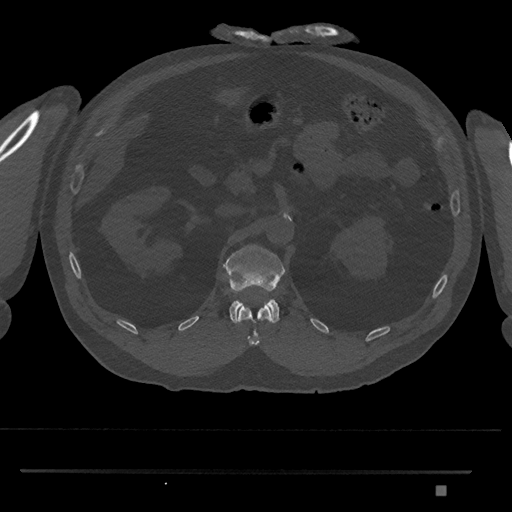
CT including the spine, one axial slice; slice 853 of 1134 in the series (ordered by position); 120 kVp; bone window (W 1800 / L 400 HU); 512 × 512 image matrix. Male patient, age 65 years. From the clinical record (not read from this slice): primary cancer: prostate.
Structures marked on this image (semi-automatic segmentation, software-assisted and operator-edited):
- L1 vertebra: box from (x=223, y=244) to (x=285, y=324) px
- T12 vertebra: (x=237, y=304)–(x=273, y=346)